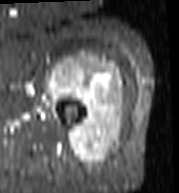
MRI of an extremity soft-tissue mass, one axial slice; slice 81 of 103 in the series (ordered by position); STIR; MR volume resampled by the dataset authors to the PET/CT grid (not the native acquisition matrix); 3.27 mm slice thickness; 179 × 193 image matrix. Female patient. From the clinical record (not read from this slice): histological type: undifferentiated – high grade; grade: high; site of the primary tumour: left thigh.
Outlined on this slice (expert contour drawn on MRI and transferred to this co-registered scan by the dataset authors):
- gross tumour volume including surrounding oedema: bounding box [x1, y1, x2, y2] px = [43, 53, 126, 170]
- gross tumour volume (mass): [45, 62, 124, 168]